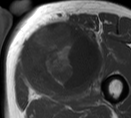
MRI of an extremity soft-tissue mass, one axial slice. Position 43 of 55 along the scan axis. MR volume resampled by the dataset authors to the PET/CT grid (not the native acquisition matrix). 3.27 mm slice thickness. 131 × 118 image matrix, field of view 128 × 115 mm. Male patient. Case-level facts recorded for this patient, not image findings: histological type: pleiomorphic liposarcoma; grade: high; site of the primary tumour: left thigh.
Structures marked on this image (expert contour drawn on MRI and transferred to this co-registered scan by the dataset authors):
- gross tumour volume including surrounding oedema: bounding box (x1, y1, x2, y2) in pixels: (20, 20, 103, 90)
- gross tumour volume (mass): (20, 23, 99, 90)